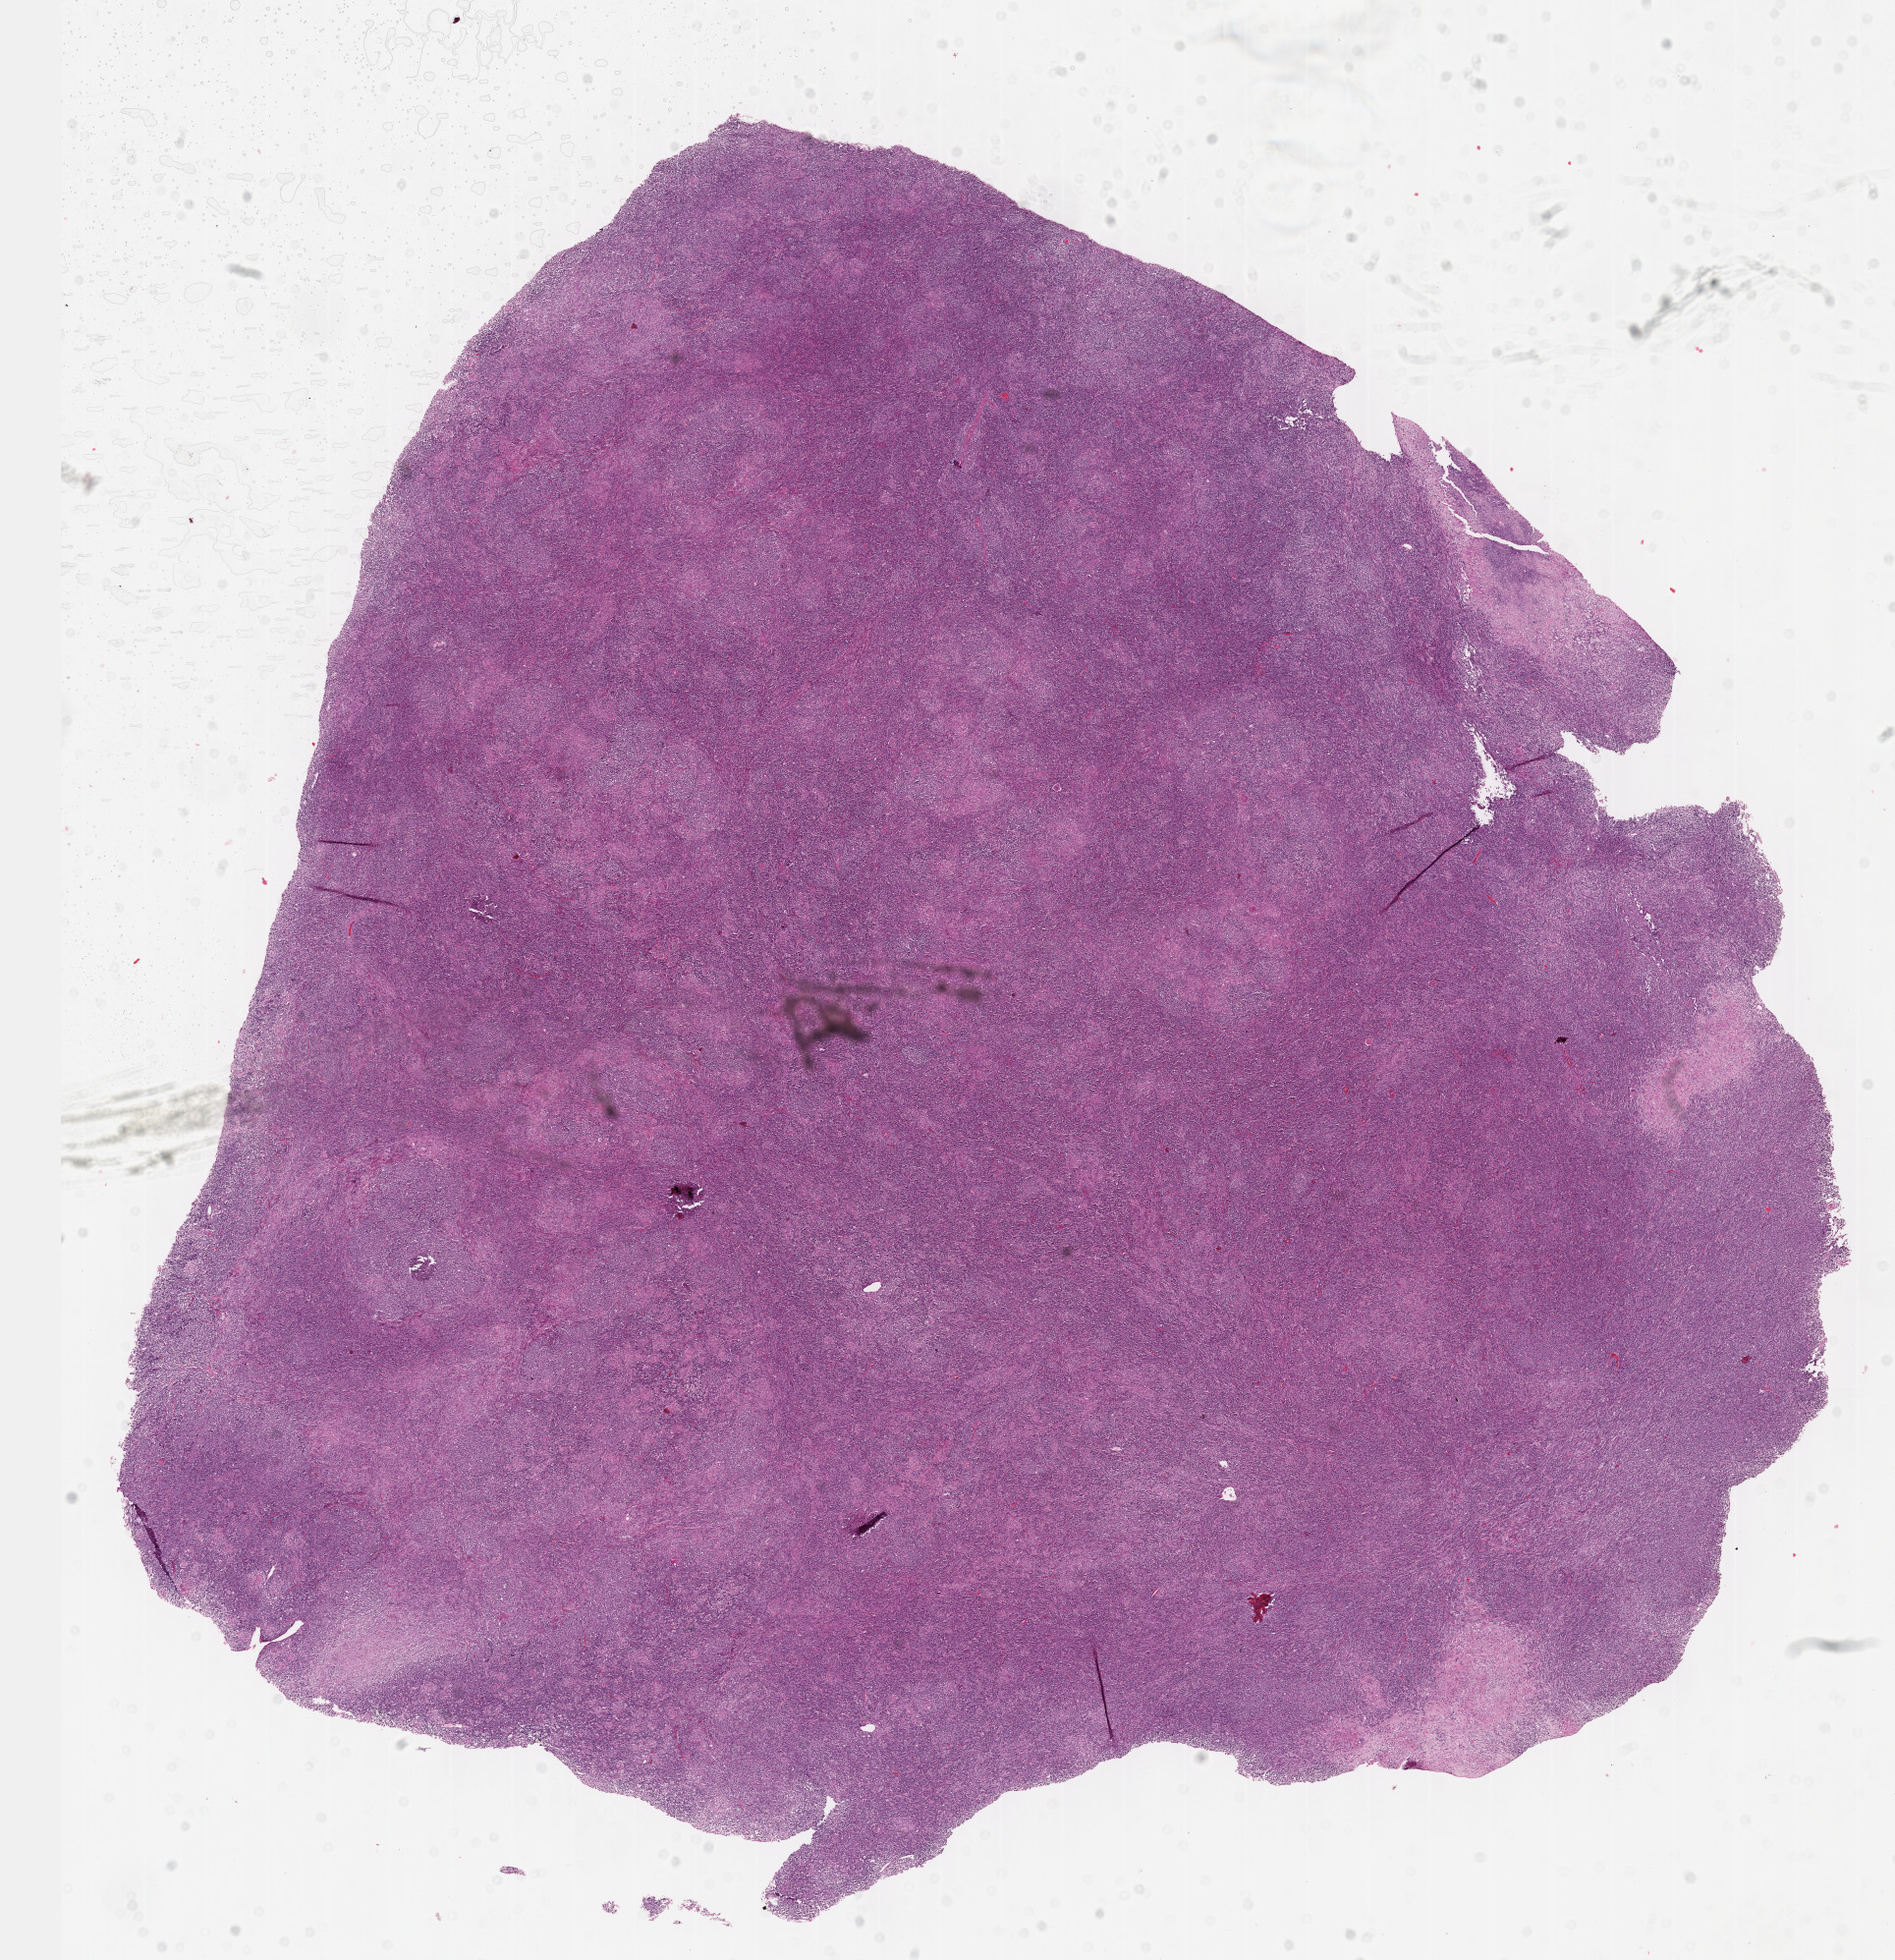
H&E-stained whole-slide image — a low-resolution overview of the entire scanned area, about 15.6 x 16.1 mm, formalin-fixed paraffin-embedded (FFPE) diagnostic section, primary tumour sample from the lymphoid tissue. Patient: female, age at initial diagnosis 77 years.
Diagnosis: Diffuse large B-cell lymphoma, NOS.